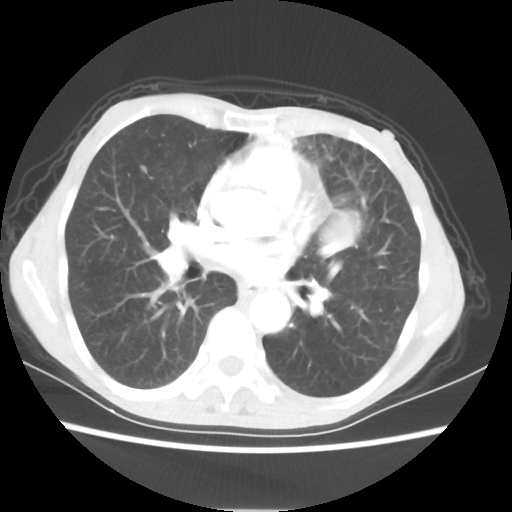
Chest CT, one axial slice. Position 30 of 56 along the scan axis. 80 kVp. Lung window (W 1500 / L -600 HU). 5 mm slice thickness. 512 × 512 image matrix. Female patient, age 60 years. Case-level facts recorded for this patient, not image findings: clinical TNM (as recorded): T4 N1 M0.
Outlined on this slice (rectangle marked by the reading radiologist):
- lung tumour (recorded histology: adenocarcinoma): bounding box (x1, y1, x2, y2) in pixels: (320, 215, 368, 256)